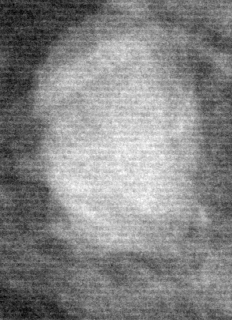
Cropped region of a digitized screen-film mammogram centred on a radiologist-marked abnormality; right breast; CC view; BI-RADS breast density category 2 (scale 1–4).
Mass, shape oval, margins circumscribed; BI-RADS assessment category 4; pathology result (as recorded, not read from the image): benign.